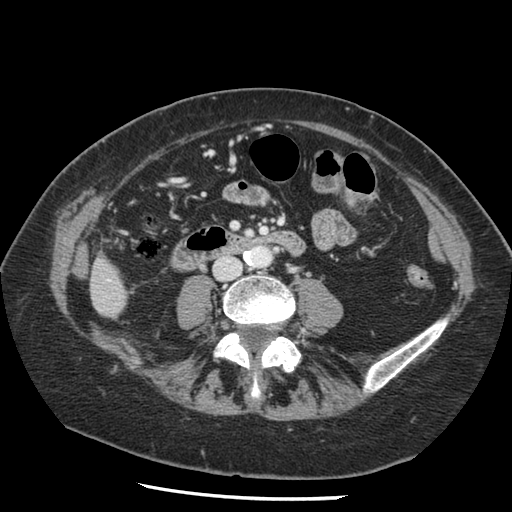
Contrast-enhanced abdominal CT, one axial slice. Position 18 of 148 along the scan axis. Intravenous contrast given. Soft-tissue window (W 400 / L 40 HU). 512 × 512 image matrix, field of view 330 × 330 mm. Female patient, age 85 years. Case-level facts recorded for this patient, not image findings: diagnosis: colorectal cancer liver metastases, imaged before liver resection; multiple liver metastases: no; largest metastasis: 0.9 cm.
Outlined on this slice (expert manual segmentation):
- liver: box from (x=91, y=260) to (x=126, y=318) px
- planned liver remnant (the part of the liver to remain after resection): (x=91, y=260)–(x=126, y=317)